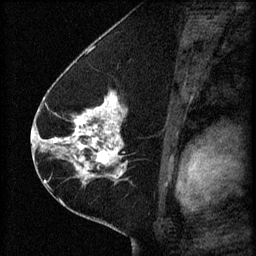
Breast MRI (dynamic contrast-enhanced), one sagittal slice; 3 images stored at this slice position (order not interpretable as contrast timing); 1.5 T; TE 4.2 ms, TR 8.2 ms; 256 × 256 image matrix, field of view 180 × 180 mm. Female patient, age 41 years.
Outlined on this slice (semi-automatic segmentation, software-assisted and operator-edited):
- analysis volume of interest (the breast-tissue region the enhancement analysis was run in; not a lesion): bounding box [x1, y1, x2, y2] px = [67, 92, 165, 173]
- tumour enhancement mask (voxels above the 70 % enhancement threshold inside the analysis volume of interest): [67, 92, 127, 173]